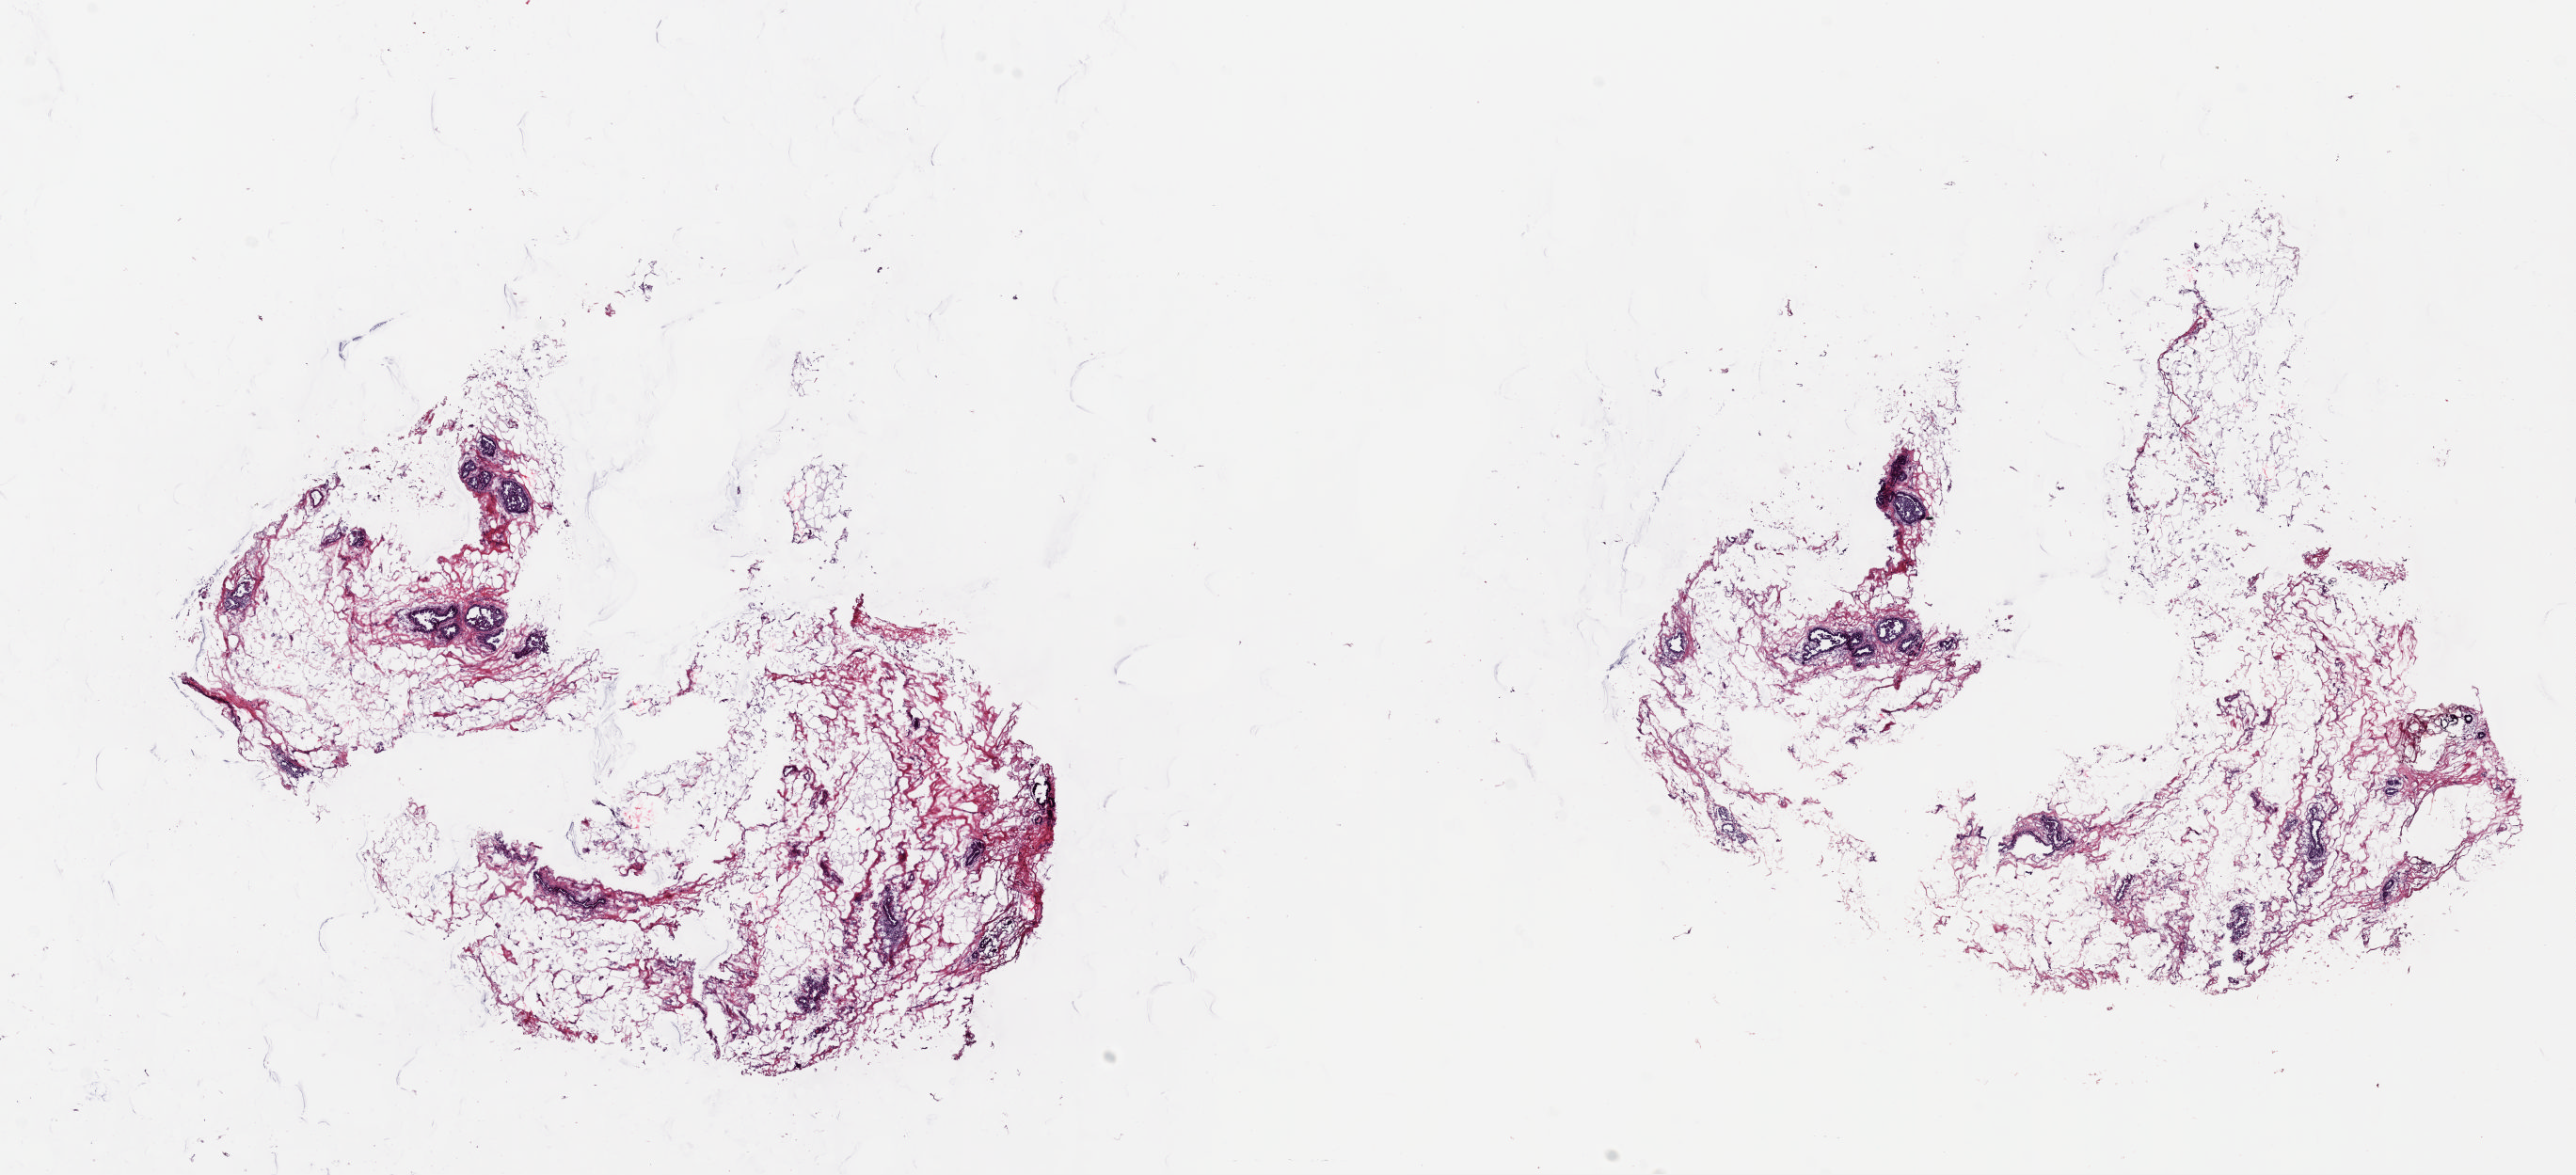
H&E-stained whole-slide image, a low-resolution overview of the entire scanned area, about 21.6 x 9.8 mm (slide scanned at 20x); frozen section from the top of the tissue portion; sample: solid tissue normal (non-tumour tissue), breast. Patient: female, age at initial diagnosis 87 years. Pathologist review of this section (percent, as recorded): tumour cells 0%, tumour nuclei 0%, normal cells 10%, stromal cells 90%, necrosis 0%. Inflammatory infiltration, as recorded: lymphocyte infiltration 0%, monocyte infiltration 0%, neutrophil infiltration 0%.
* this section: solid tissue normal sample (biorepository sample class)
* patient diagnosis: Lobular carcinoma, NOS